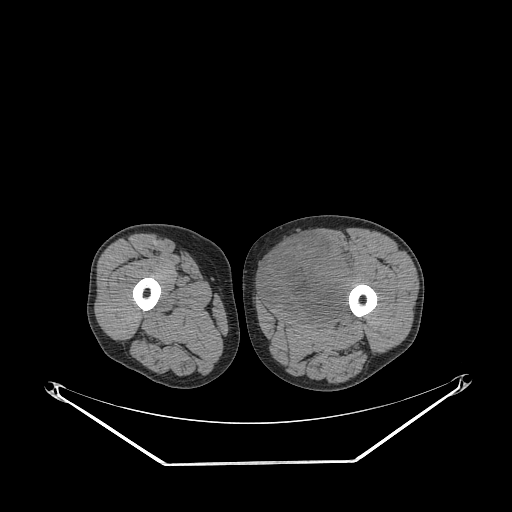
CT of an extremity soft-tissue mass (from a PET/CT study), one axial slice; position 245 of 267 along the scan axis; reconstruction kernel STANDARD; soft-tissue window (W 400 / L 40 HU); 3.75 mm slice thickness; 512 × 512 image matrix. Male patient. Case-level facts recorded for this patient, not image findings: histological type: pleiomorphic liposarcoma; grade: high; site of the primary tumour: left thigh.
Structures marked on this image (expert contour drawn on MRI and transferred to this co-registered scan by the dataset authors):
- gross tumour volume including surrounding oedema: bounding box [x1, y1, x2, y2] px = [262, 233, 357, 318]
- gross tumour volume (mass): [263, 235, 353, 320]